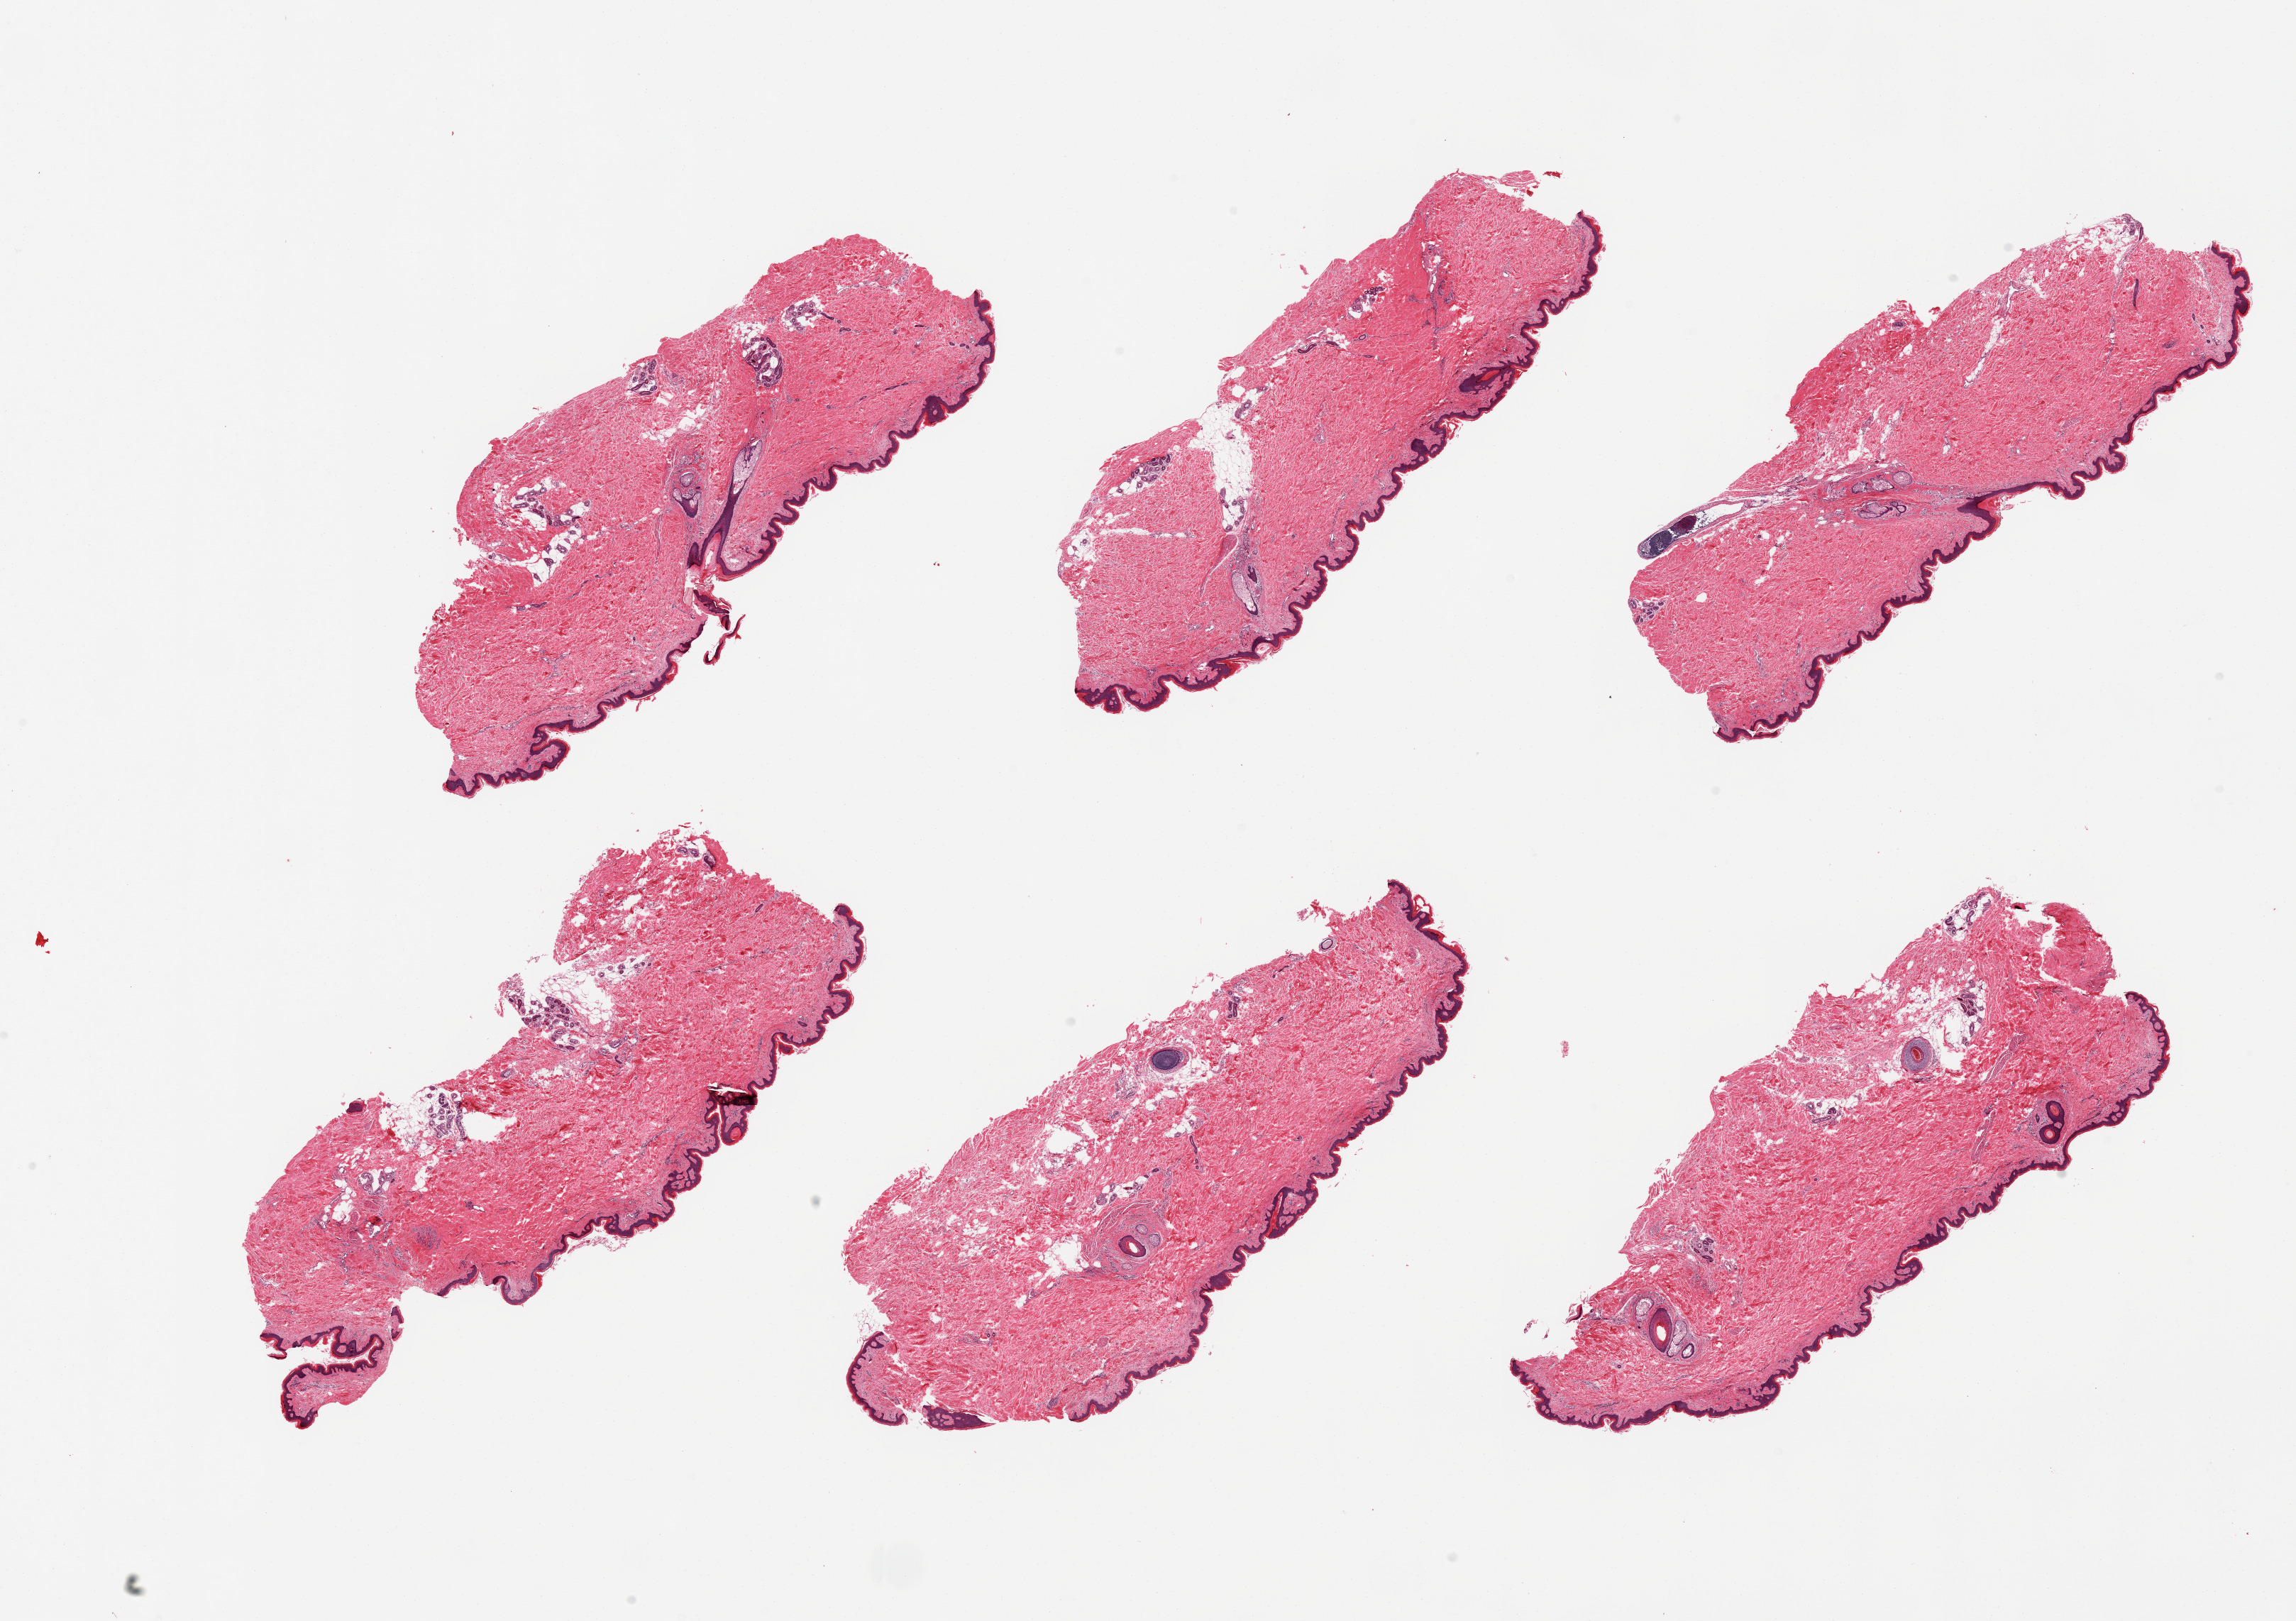
Digitized H&E-stained section, brightfield, shown as a low-resolution overview of the whole scanned area (about 25.6 x 18.1 mm). PAXgene-fixed, paraffin-embedded tissue. Section of skin of suprapubic region (target tissue). Tissue donor sample. Donor sex: male.
• review note (as recorded): 6 pieces, minimal adherent fat; squamous mucosa is ~60-70 microns